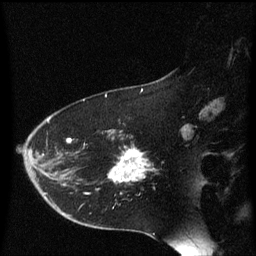
Breast MRI (dynamic contrast-enhanced), one sagittal slice. Slice 40 of 60 in the series (ordered by position). Dynamic contrast-enhanced series, image 2 of 3 at this slice position (ordered by acquisition). 1.5 T. TE 4.2 ms, TR 8.4 ms. 2 mm slice thickness. 256 × 256 image matrix, field of view 200 × 200 mm. Female patient, age 54 years. Case-level facts recorded for this patient, not image findings: setting: breast cancer imaged before/during neoadjuvant chemotherapy; receptor status: HR-positive, HER2-negative.
Structures marked on this image (semi-automatic segmentation, software-assisted and operator-edited):
- analysis volume of interest (the breast-tissue region the enhancement analysis was run in; not a lesion): bounding box (x1, y1, x2, y2) in pixels: (109, 130, 150, 185)
- tumour enhancement mask (voxels above the 70 % enhancement threshold inside the analysis volume of interest): (112, 148, 150, 183)